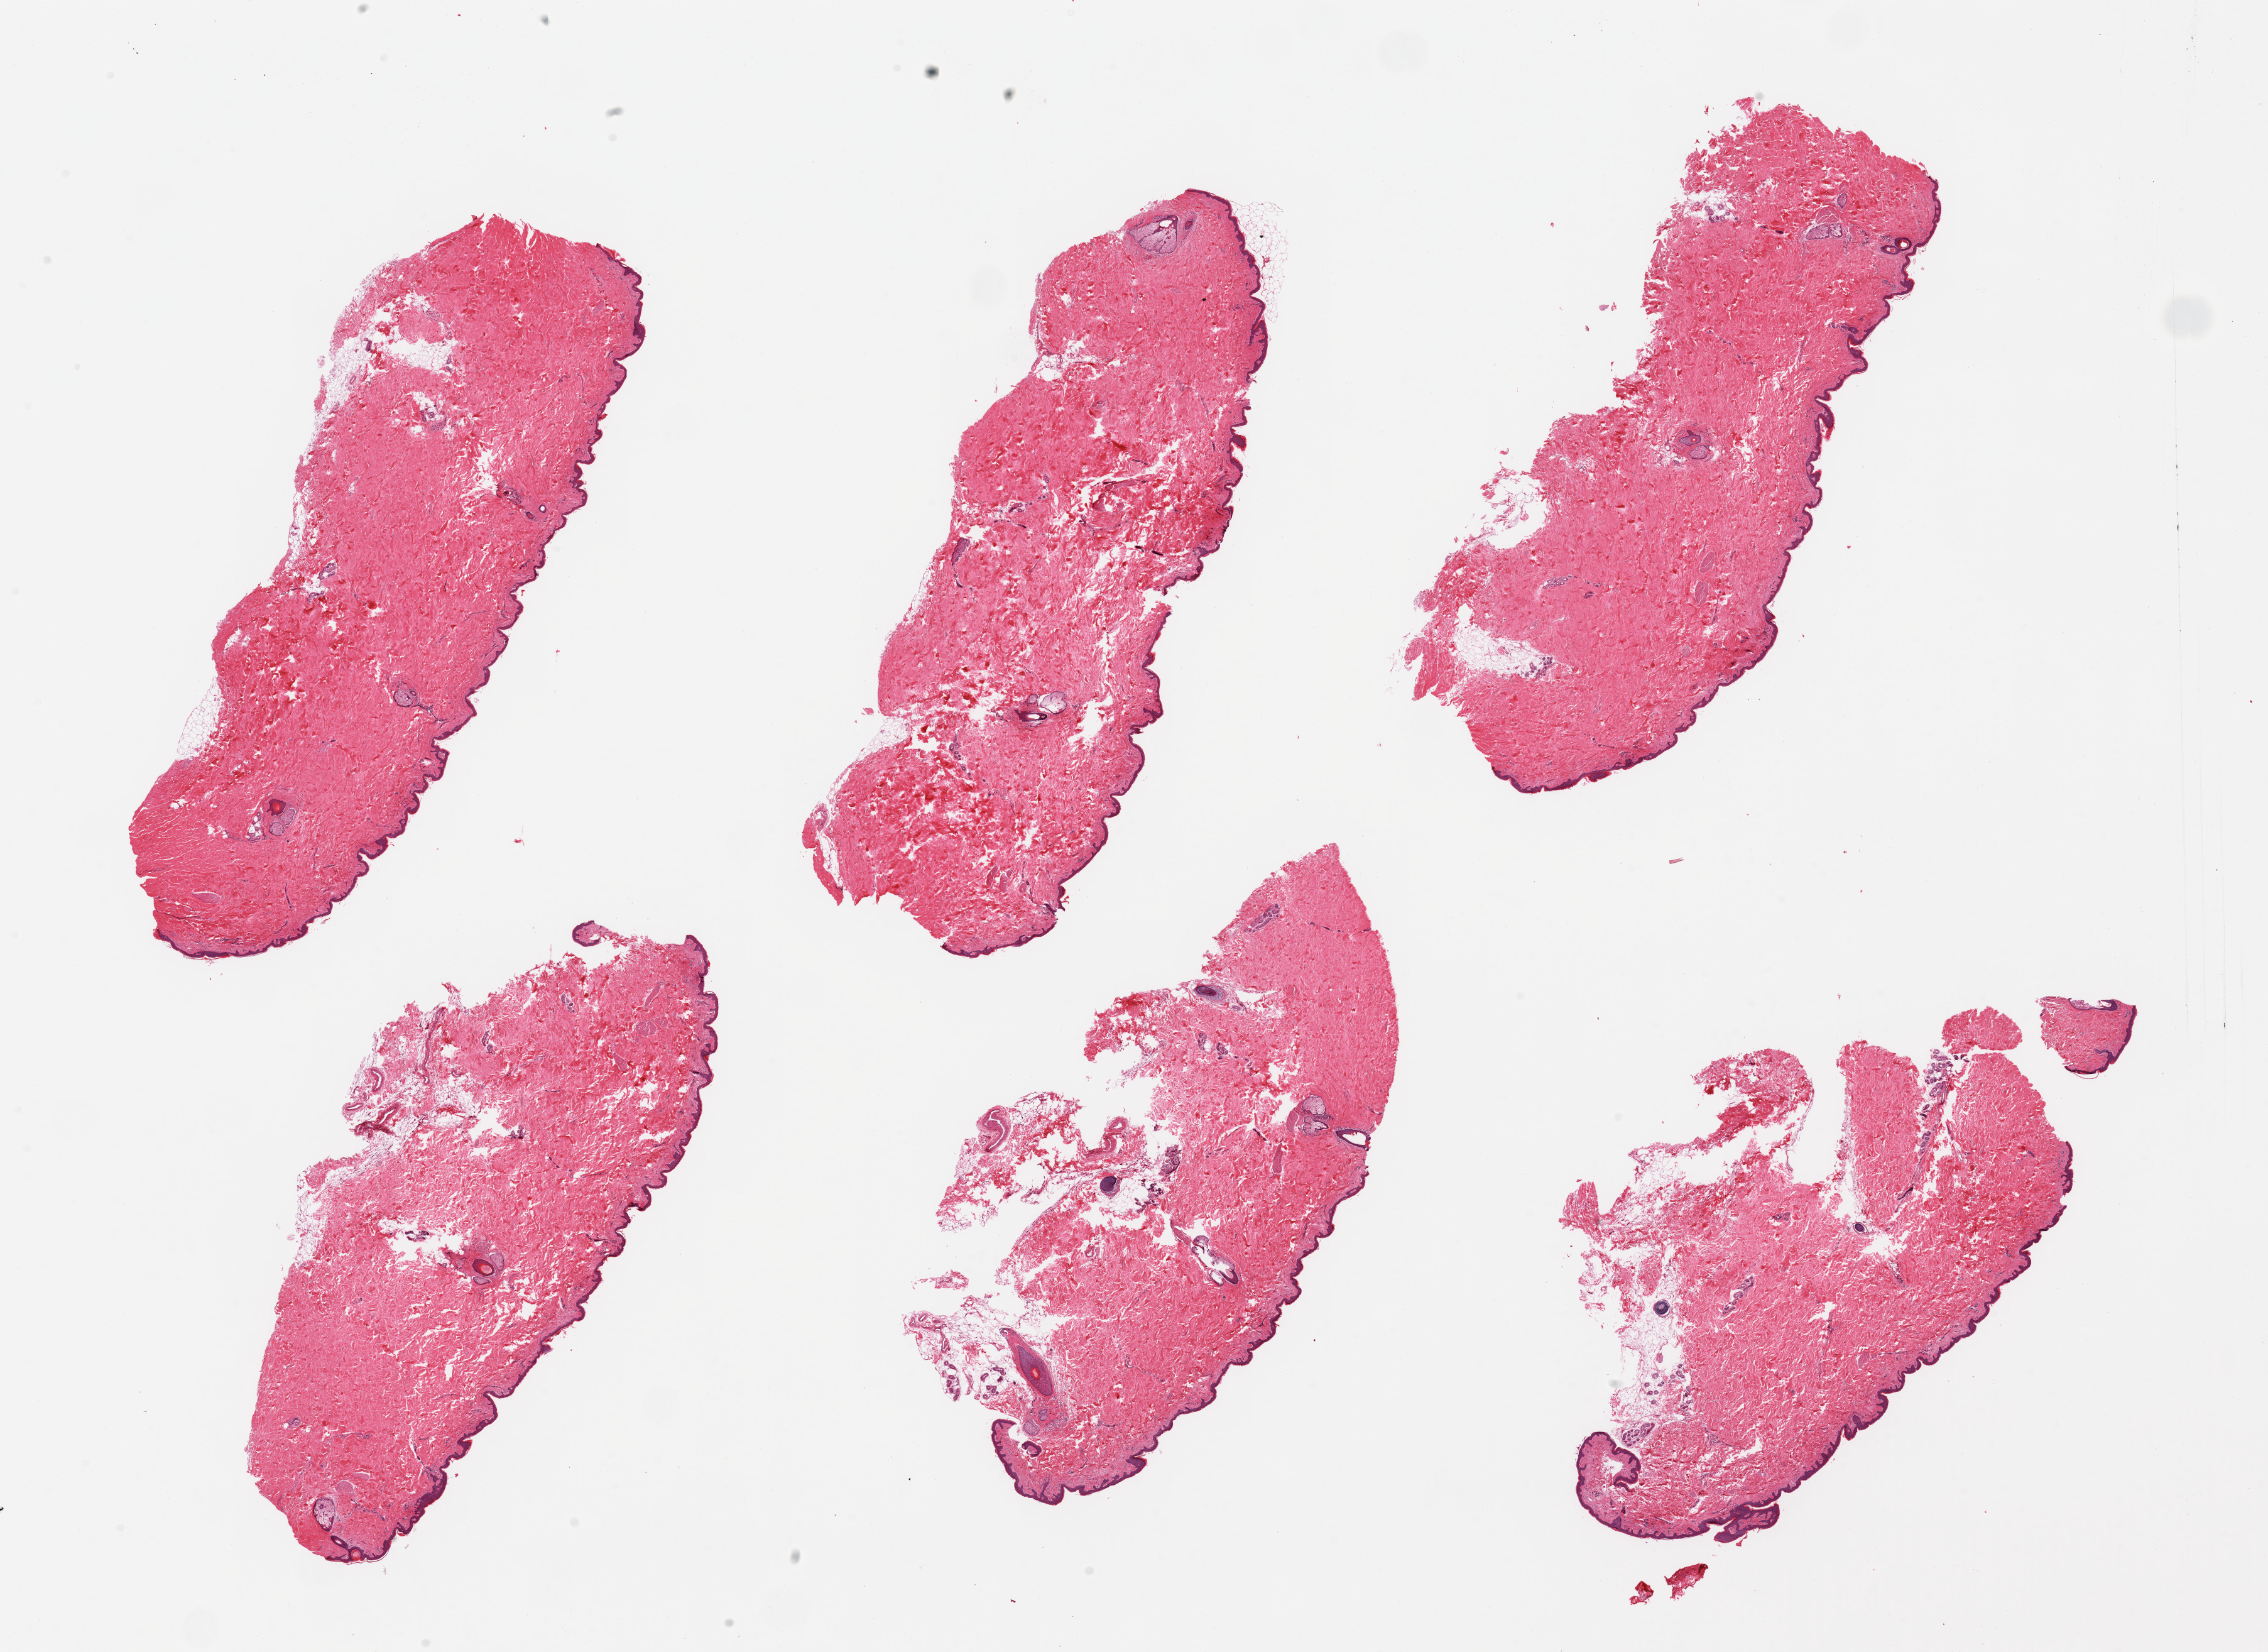
Digitized haematoxylin and eosin-stained section — a low-resolution overview of the entire scanned area, about 28.5 x 20.8 mm; PAXgene-fixed, paraffin-embedded tissue; section of skin of suprapubic region (target tissue); tissue donor sample.
- review note (as recorded): 6 pieces, no dermal fat; squamous epithelium is ~35-40 microns